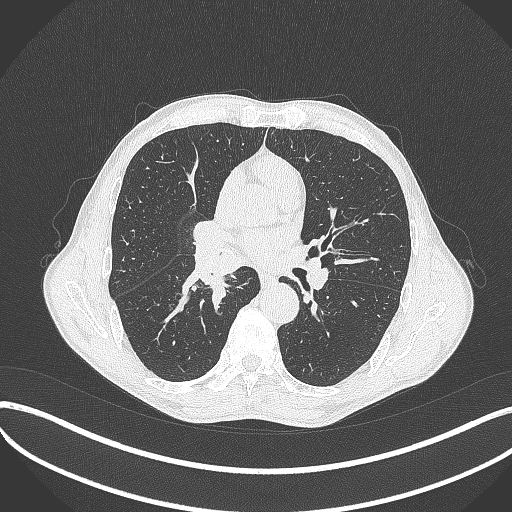
Chest CT, one axial slice; slice 232 of 481 in the series (ordered by position); 120 kVp; lung window (W 1500 / L -600 HU); 1 mm slice thickness; 512 × 512 image matrix. Male patient, age 65 years. From the clinical record (not read from this slice): clinical TNM (as recorded): T2a N0 M0; histopathological grade: G2.
Outlined on this slice (bounding box drawn by a radiologist):
- lung tumour (recorded histology: squamous cell carcinoma): bounding box [x1, y1, x2, y2] px = [186, 219, 246, 293]